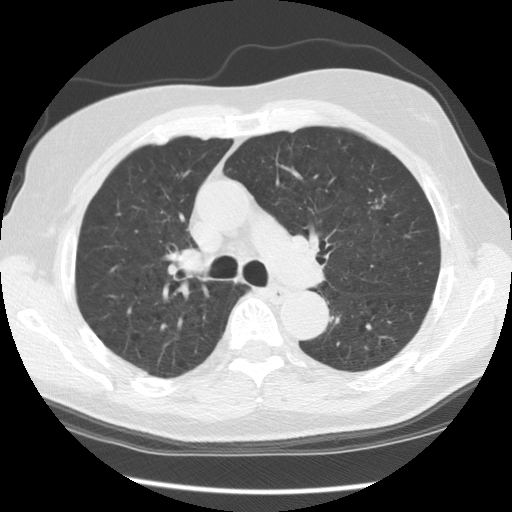
Chest CT (low-dose screening protocol), one axial image. Second screening round (one year after baseline). Lung window (W 1500 / L -600 HU). 140 kVp. Slice 90 of 140 in the series. Male participant, aged 70 years at enrolment. Current smoker at enrolment.
Expert reader's lesion annotation, bounding box (x1, y1, x2, y2) in pixels: (343, 182, 404, 237). The screening reader recorded 3 non-calcified nodules or masses ≥4 mm on this exam (right lower lobe, left upper lobe, left upper lobe); which of them this box marks is not recorded. Official screen result: positive, other.